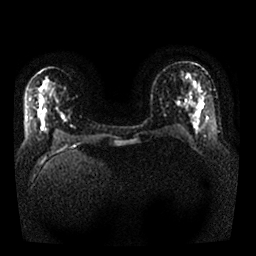
Breast MRI, one axial slice. Position 16 of 25 along the scan axis. Diffusion-weighted series; image 2 of 4 stored at this slice position (different b-values; order by instance number). 1.5 T. 4 mm slice thickness. 256 × 256 image matrix, field of view 340 × 340 mm. Female patient.
Outlined on this slice (manually delineated by an expert):
- tumour on diffusion-weighted imaging: bounding box (x1, y1, x2, y2) in pixels: (194, 102, 204, 119)